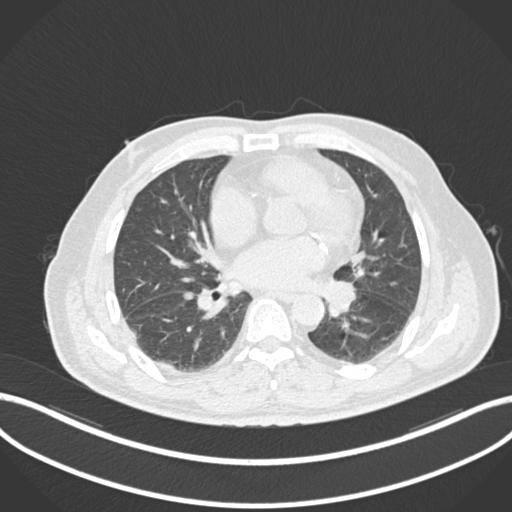
Chest CT, one axial slice; slice 61 of 161 in the series (ordered by position); reconstruction kernel B30f; lung window (W 1500 / L -600 HU); 1 mm slice thickness; 512 × 512 image matrix, field of view 400 × 400 mm. Male patient, age 71 years. Case-level facts recorded for this patient, not image findings: clinical TNM (as recorded): T1b N0 M0.
Structures marked on this image (bounding box drawn by a radiologist):
- lung tumour (recorded histology: squamous cell carcinoma): bounding box [x1, y1, x2, y2] px = [324, 279, 359, 318]